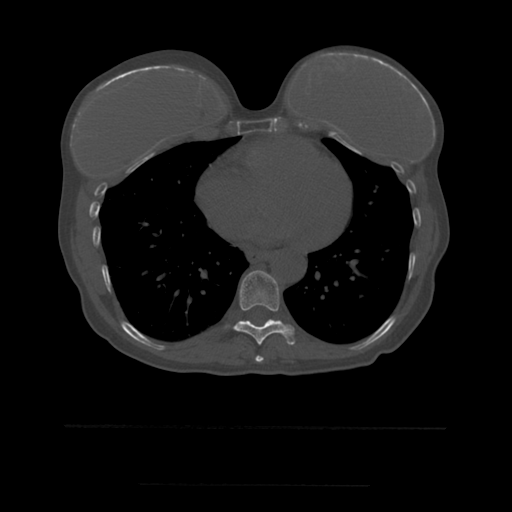
CT including the spine, one axial slice; position 319 of 544 along the scan axis; bone window (W 1800 / L 400 HU); 1.25 mm slice thickness; 512 × 512 image matrix, field of view 350 × 350 mm. Patient age 58 years. From the clinical record (not read from this slice): primary cancer: lung.
Annotated regions visible in this slice (semi-automatic segmentation, software-assisted and operator-edited):
- T8 vertebra: bounding box <256,356,264,363> (left, top, right, bottom; pixels)
- T9 vertebra: <234,271,295,345>